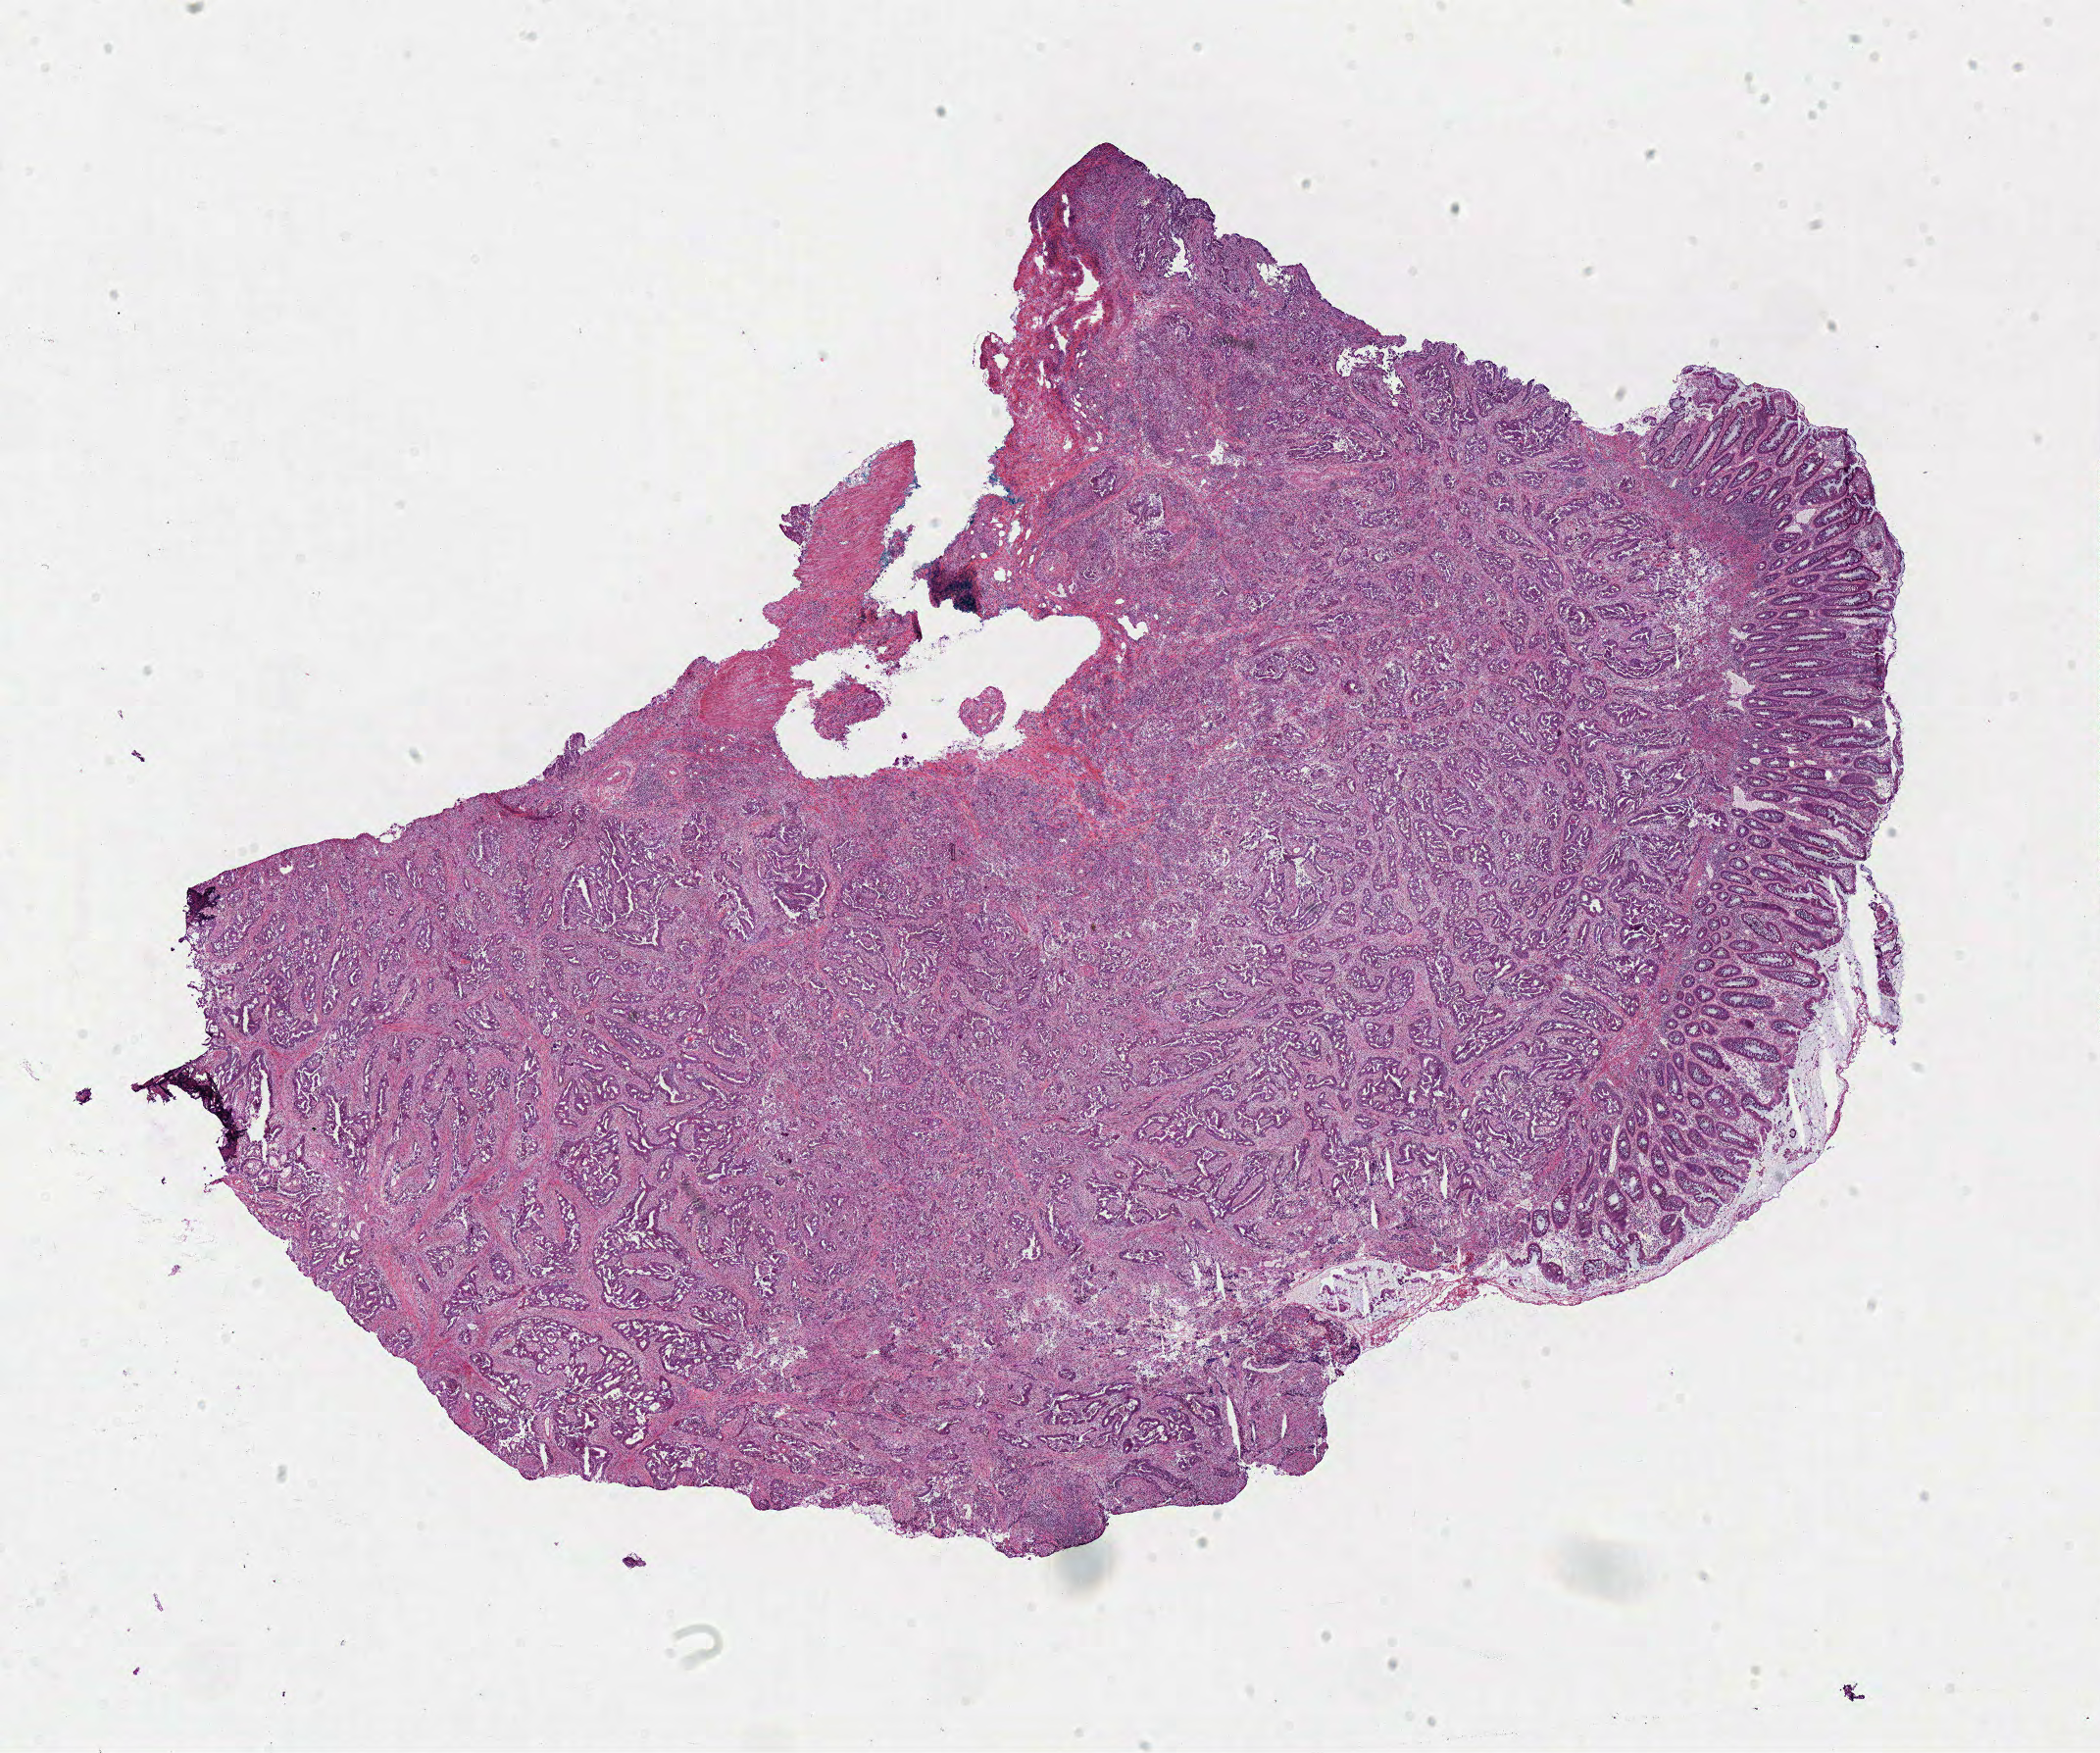
H&E-stained whole-slide image, whole scanned area (about 16.9 x 14.1 mm, acquisition: 40x scan) shown as a low-resolution overview; frozen section from the bottom of the tissue portion; rectum, primary tumour sample. Male, age 70 years at initial diagnosis. Composition of this section per pathologist review: tumour cells 67%, tumour nuclei 70%, normal cells 8%, stromal cells 20%, necrosis 5%.
Lymph nodes positive (case pathology): 0 of 1 examined. AJCC pathologic stage: I. Diagnosis: Adenocarcinoma, NOS.